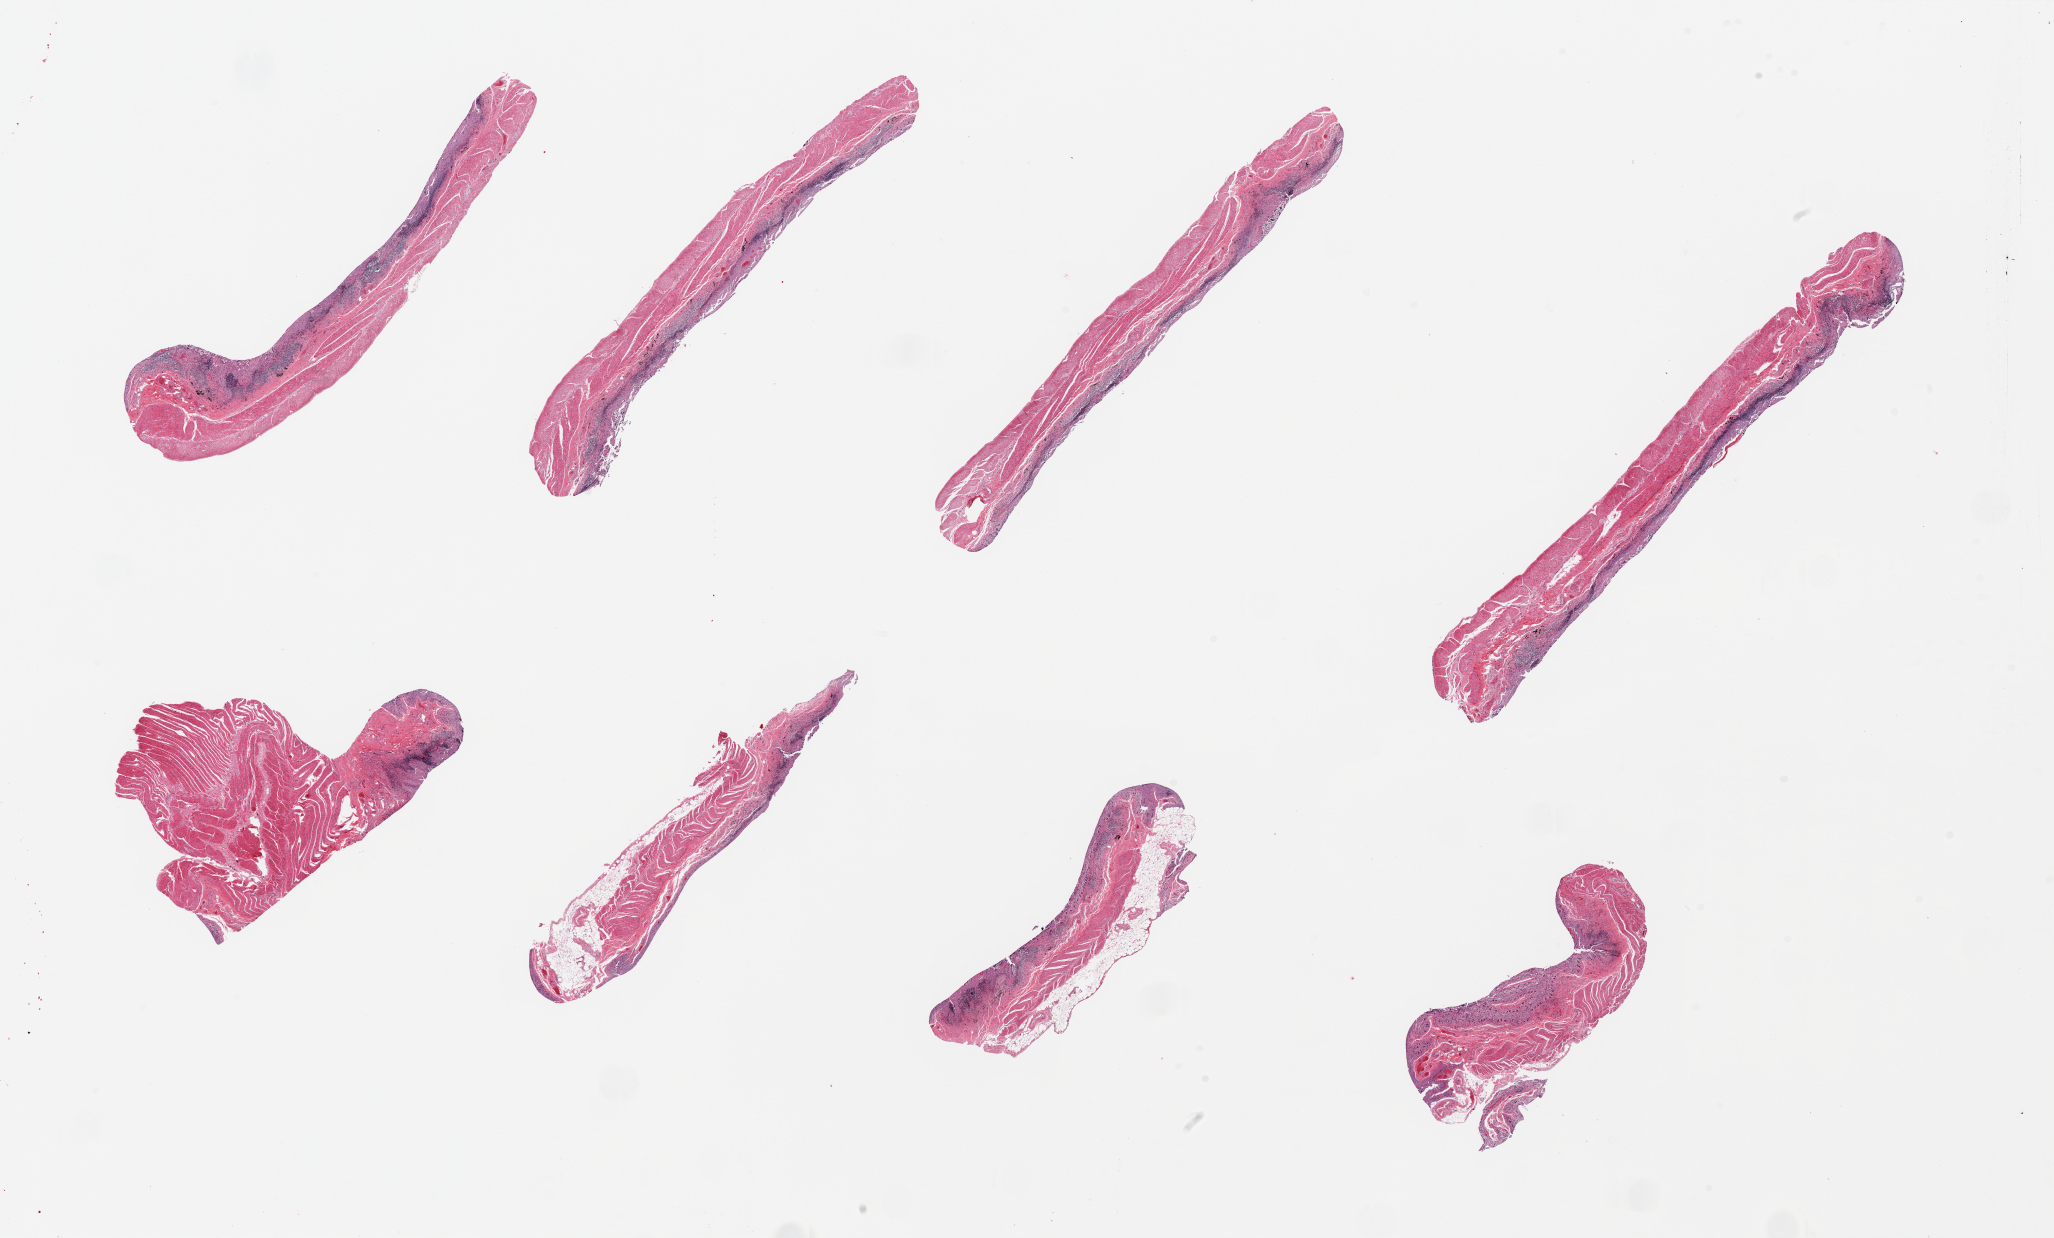
Digitized hematoxylin and eosin (H&E)-stained section, brightfield, shown as a low-resolution overview of the whole scanned area (about 32.5 x 19.6 mm, acquisition: 20x scan). PAXgene-fixed paraffin-embedded (PFPE) section. Sampled site (target tissue): ileum. Donor tissue sample. Male donor.
Review note (as recorded): 6 pieces, glandular mucosa completely autolyzed/sloughed; residcual lymphoid aggegates 10-15% tissue.